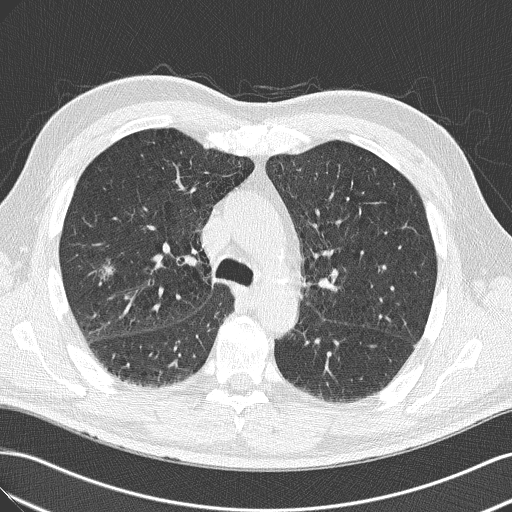
Low-dose screening chest CT, one axial slice. Slice 89 of 143 in the series (ordered by position). Lung window (W 1500 / L -600 HU). 512 × 512 image matrix, field of view 360 × 360 mm.
Structures marked on this image (expert manual segmentation):
- lesion 1 (tumor, lower lobe of right lung): bounding box (x1, y1, x2, y2) in pixels: (101, 265, 114, 279)